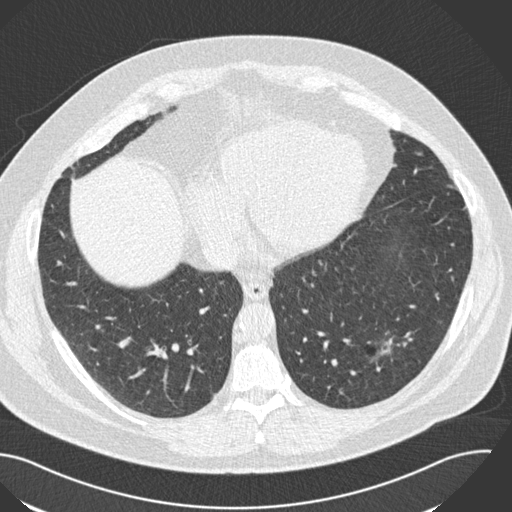
Chest CT (low-dose screening protocol), one axial image. Third screening round (two years after baseline). Lung window (W 1500 / L -600 HU). Slice 91 of 153 in the series. Male, age 57 years at enrolment. Current smoker at enrolment.
Lesion marked by an expert reader, bounding box <349,318,427,381> (left, top, right, bottom; pixels). The exam's reader record, not a measurement of the box and not confirmed to be the same lesion: non-calcified nodule or mass ≥4 mm, left lower lobe, 22 × 18 mm, poorly defined margins, soft tissue attenuation, pre-existing on the prior screen: yes; interval growth: yes. Official screen result: positive, other. Participant outcome: lung cancer diagnosed 124 days after this screen — squamous cell carcinoma, NOS, left lower lobe, moderately differentiated (G2), stage IA (AJCC 6th edition), 22 mm at pathology.